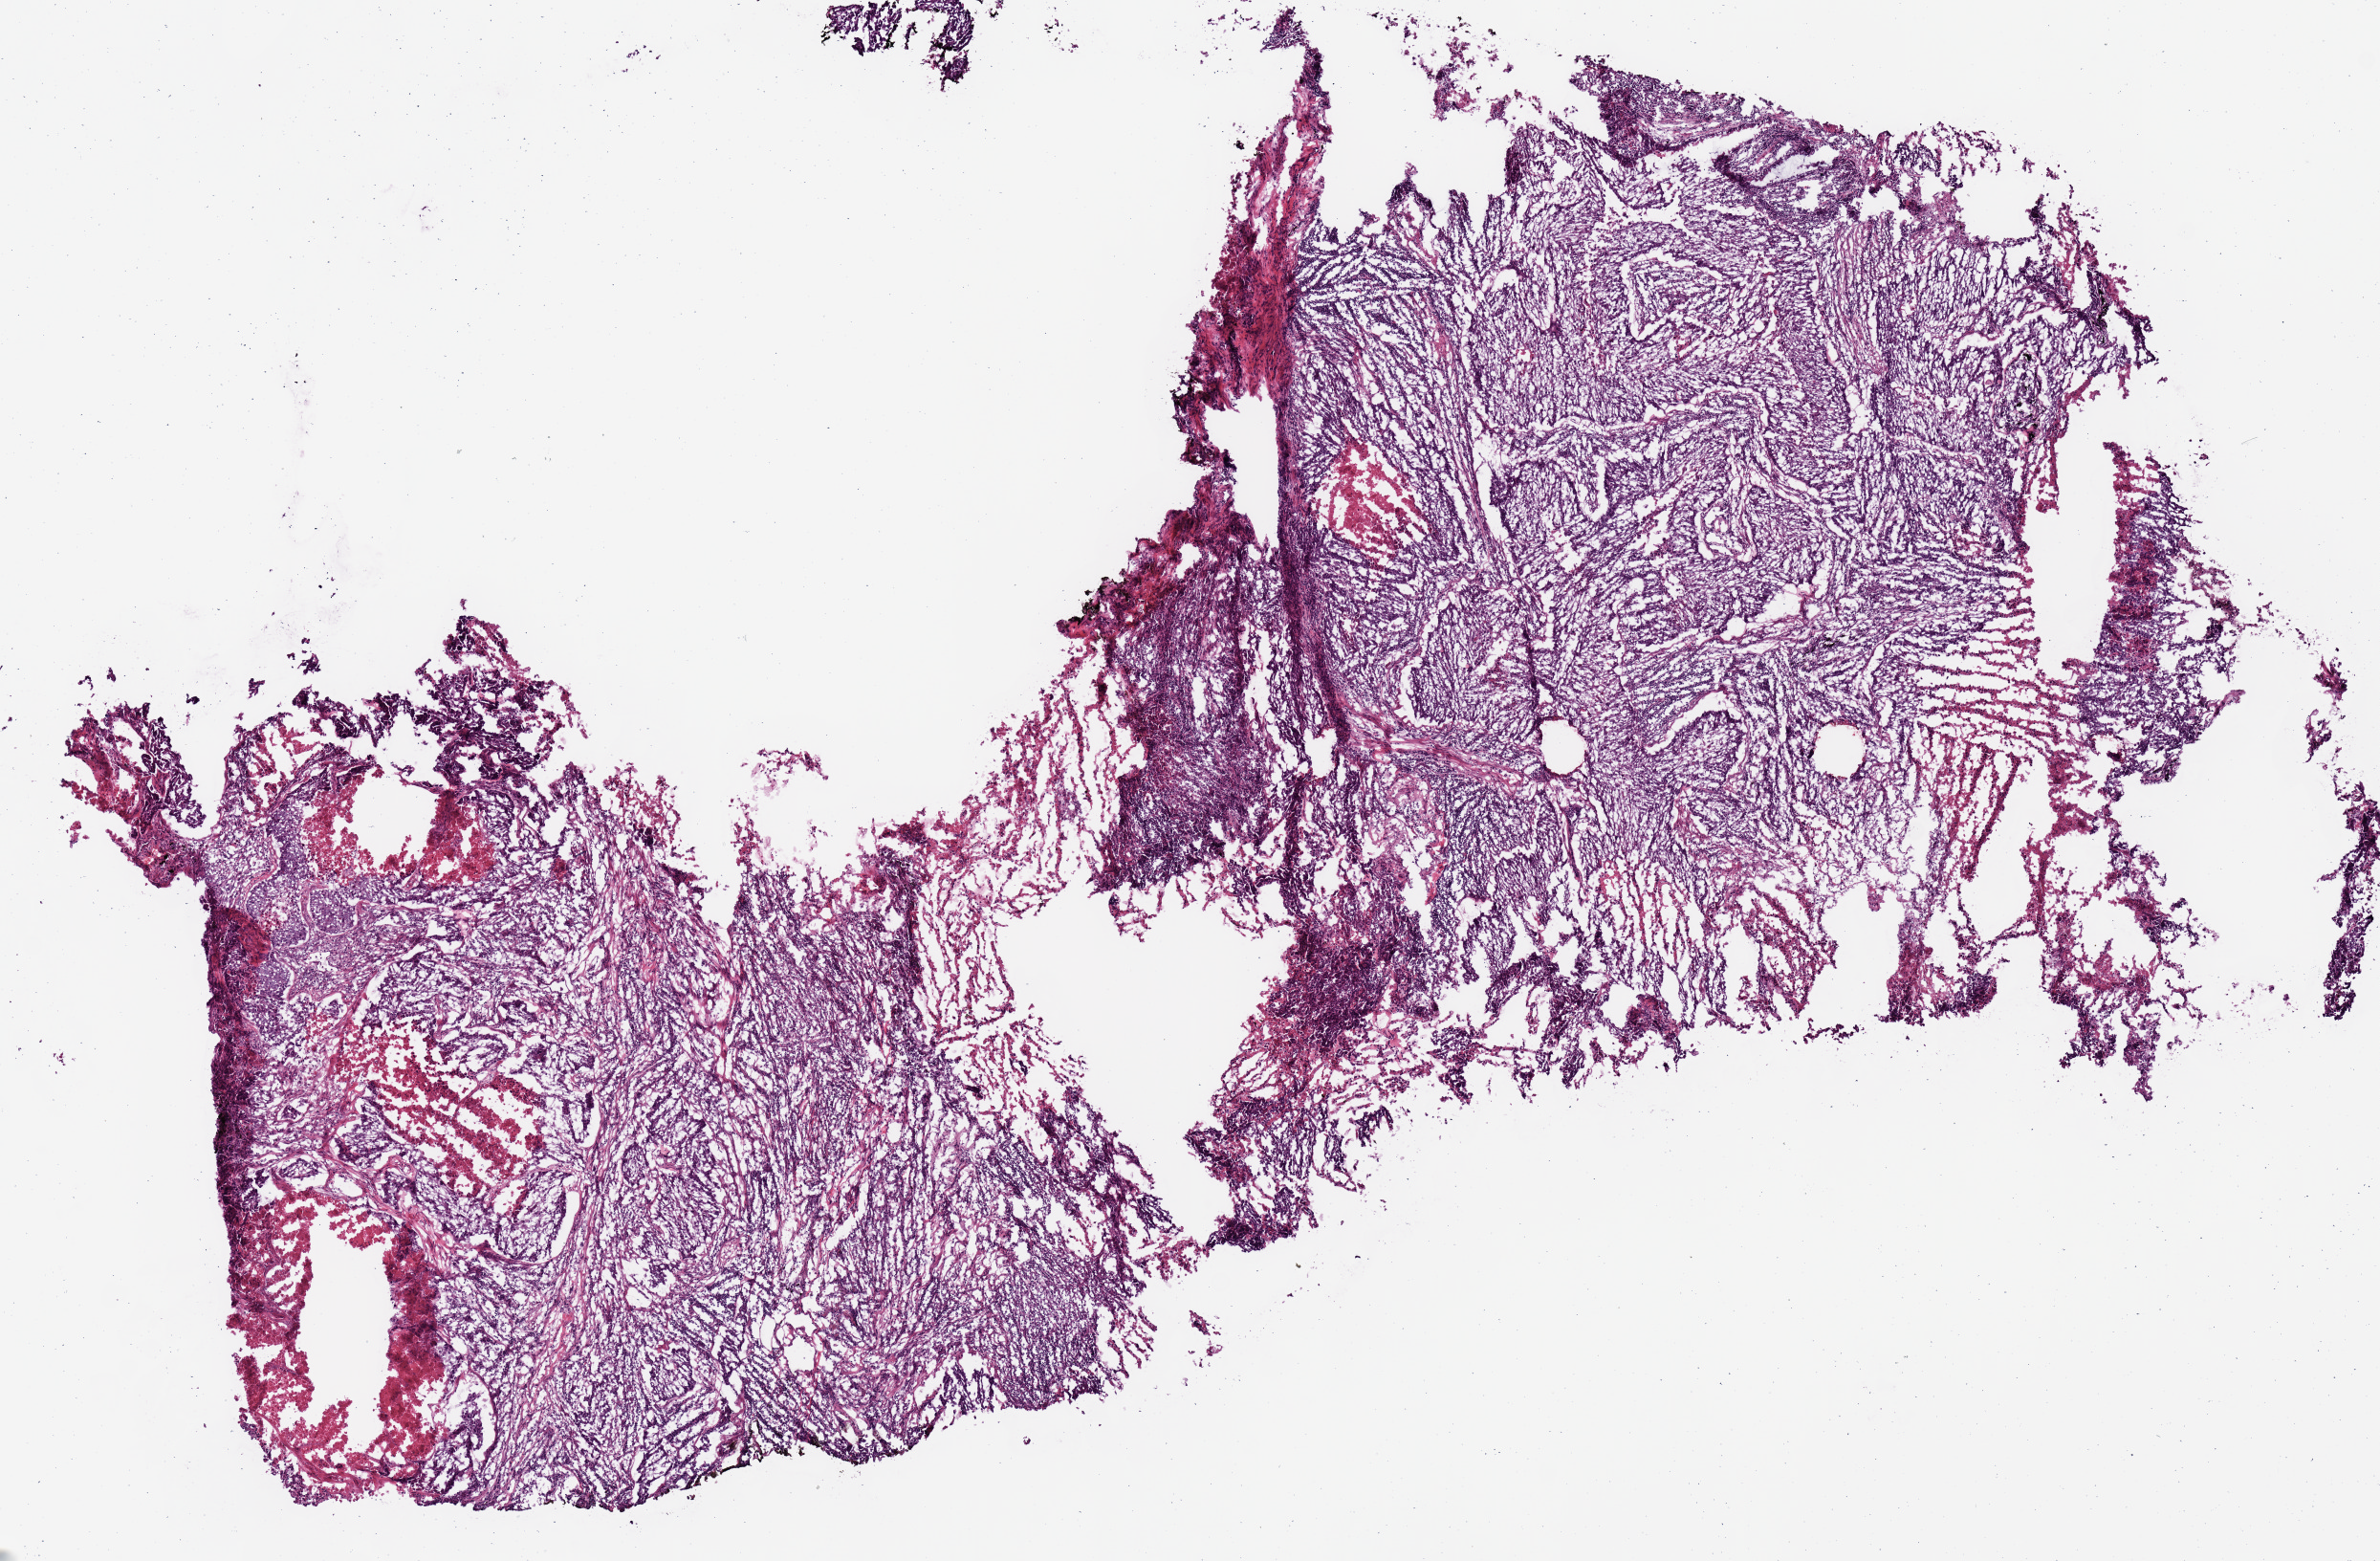
H&E whole-slide image, low-resolution overview of the scanned area, about 9.8 x 6.5 mm (acquisition: 20x scan); frozen section from the top of the tissue portion; lung, primary tumour sample. Patient: male, age at initial diagnosis 60 years. Composition of this section per pathologist review: tumour cells 77%, tumour nuclei 60%, normal cells 0%, stromal cells 15%, necrosis 8%.
AJCC pathologic stage: IB (7th edition). TNM: T2a N0 M0. Pathologic diagnosis: Squamous cell carcinoma, NOS (upper lobe, lung). Laterality: left.